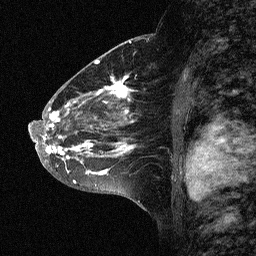
Breast MRI (dynamic contrast-enhanced), one sagittal slice; position 35 of 64 along the scan axis; dynamic contrast-enhanced study with each time point stored as its own series, time point 2 of 3 at this slice position (early post-contrast, ordered by acquisition time); 1.5 T; TE 4.5 ms, TR 11 ms; 2.06 mm slice thickness; 256 × 256 image matrix. Female patient, age 46 years. Case-level facts recorded for this patient, not image findings: setting: breast cancer imaged before/during neoadjuvant chemotherapy; receptor status: HER2-positive.
Annotated regions visible in this slice (semi-automatically segmented with operator editing):
- analysis volume of interest (the breast-tissue region the enhancement analysis was run in; not a lesion): bounding box [x1, y1, x2, y2] px = [43, 72, 165, 177]
- tumour enhancement mask (voxels above the 90 % enhancement threshold inside the analysis volume of interest): [43, 76, 137, 175]